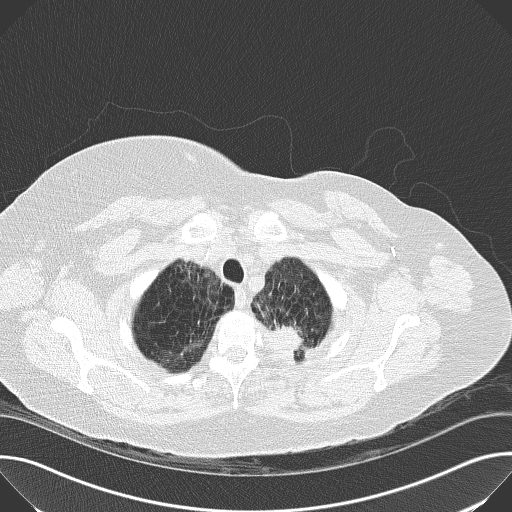
Chest CT (low-dose screening protocol), one axial image, baseline annual screen, lung window (W 1500 / L -600 HU), 2 mm slice thickness, 120 kVp, slice 150 of 169 in the series, 512 × 512 image matrix, field of view 380 × 380 mm. Female, age 56 years at enrolment. Current smoker at enrolment.
- Expert reader's lesion annotation, bounding box [x1, y1, x2, y2] px = [254, 304, 320, 366].
- Screening reader's record for this exam (one nodule recorded; not confirmed to be the boxed lesion): non-calcified nodule or mass ≥4 mm, left upper lobe, 19 × 17 mm, spiculated (stellate) margins, soft tissue attenuation.
- Participant outcome: lung cancer diagnosed 70 days after this screen — mucin-producing adenocarcinoma, left upper lobe, well differentiated (G1), stage IIB (AJCC 6th edition), 30 mm at pathology.